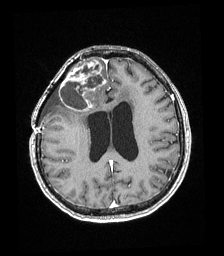
Brain MRI from a brain-tumour surgery series, one axial slice. Slice 79 of 192 in the series (ordered by position). T1-weighted post-contrast. 1 mm slice thickness. 224 × 256 image matrix, field of view 219 × 250 mm. Case-level facts recorded for this patient, not image findings: histopathology: Astrocytoma; WHO grade: 4; IDH mutation: yes.
Annotated regions visible in this slice (expert manual segmentation):
- tumour: bounding box [x1, y1, x2, y2] px = [59, 61, 105, 112]